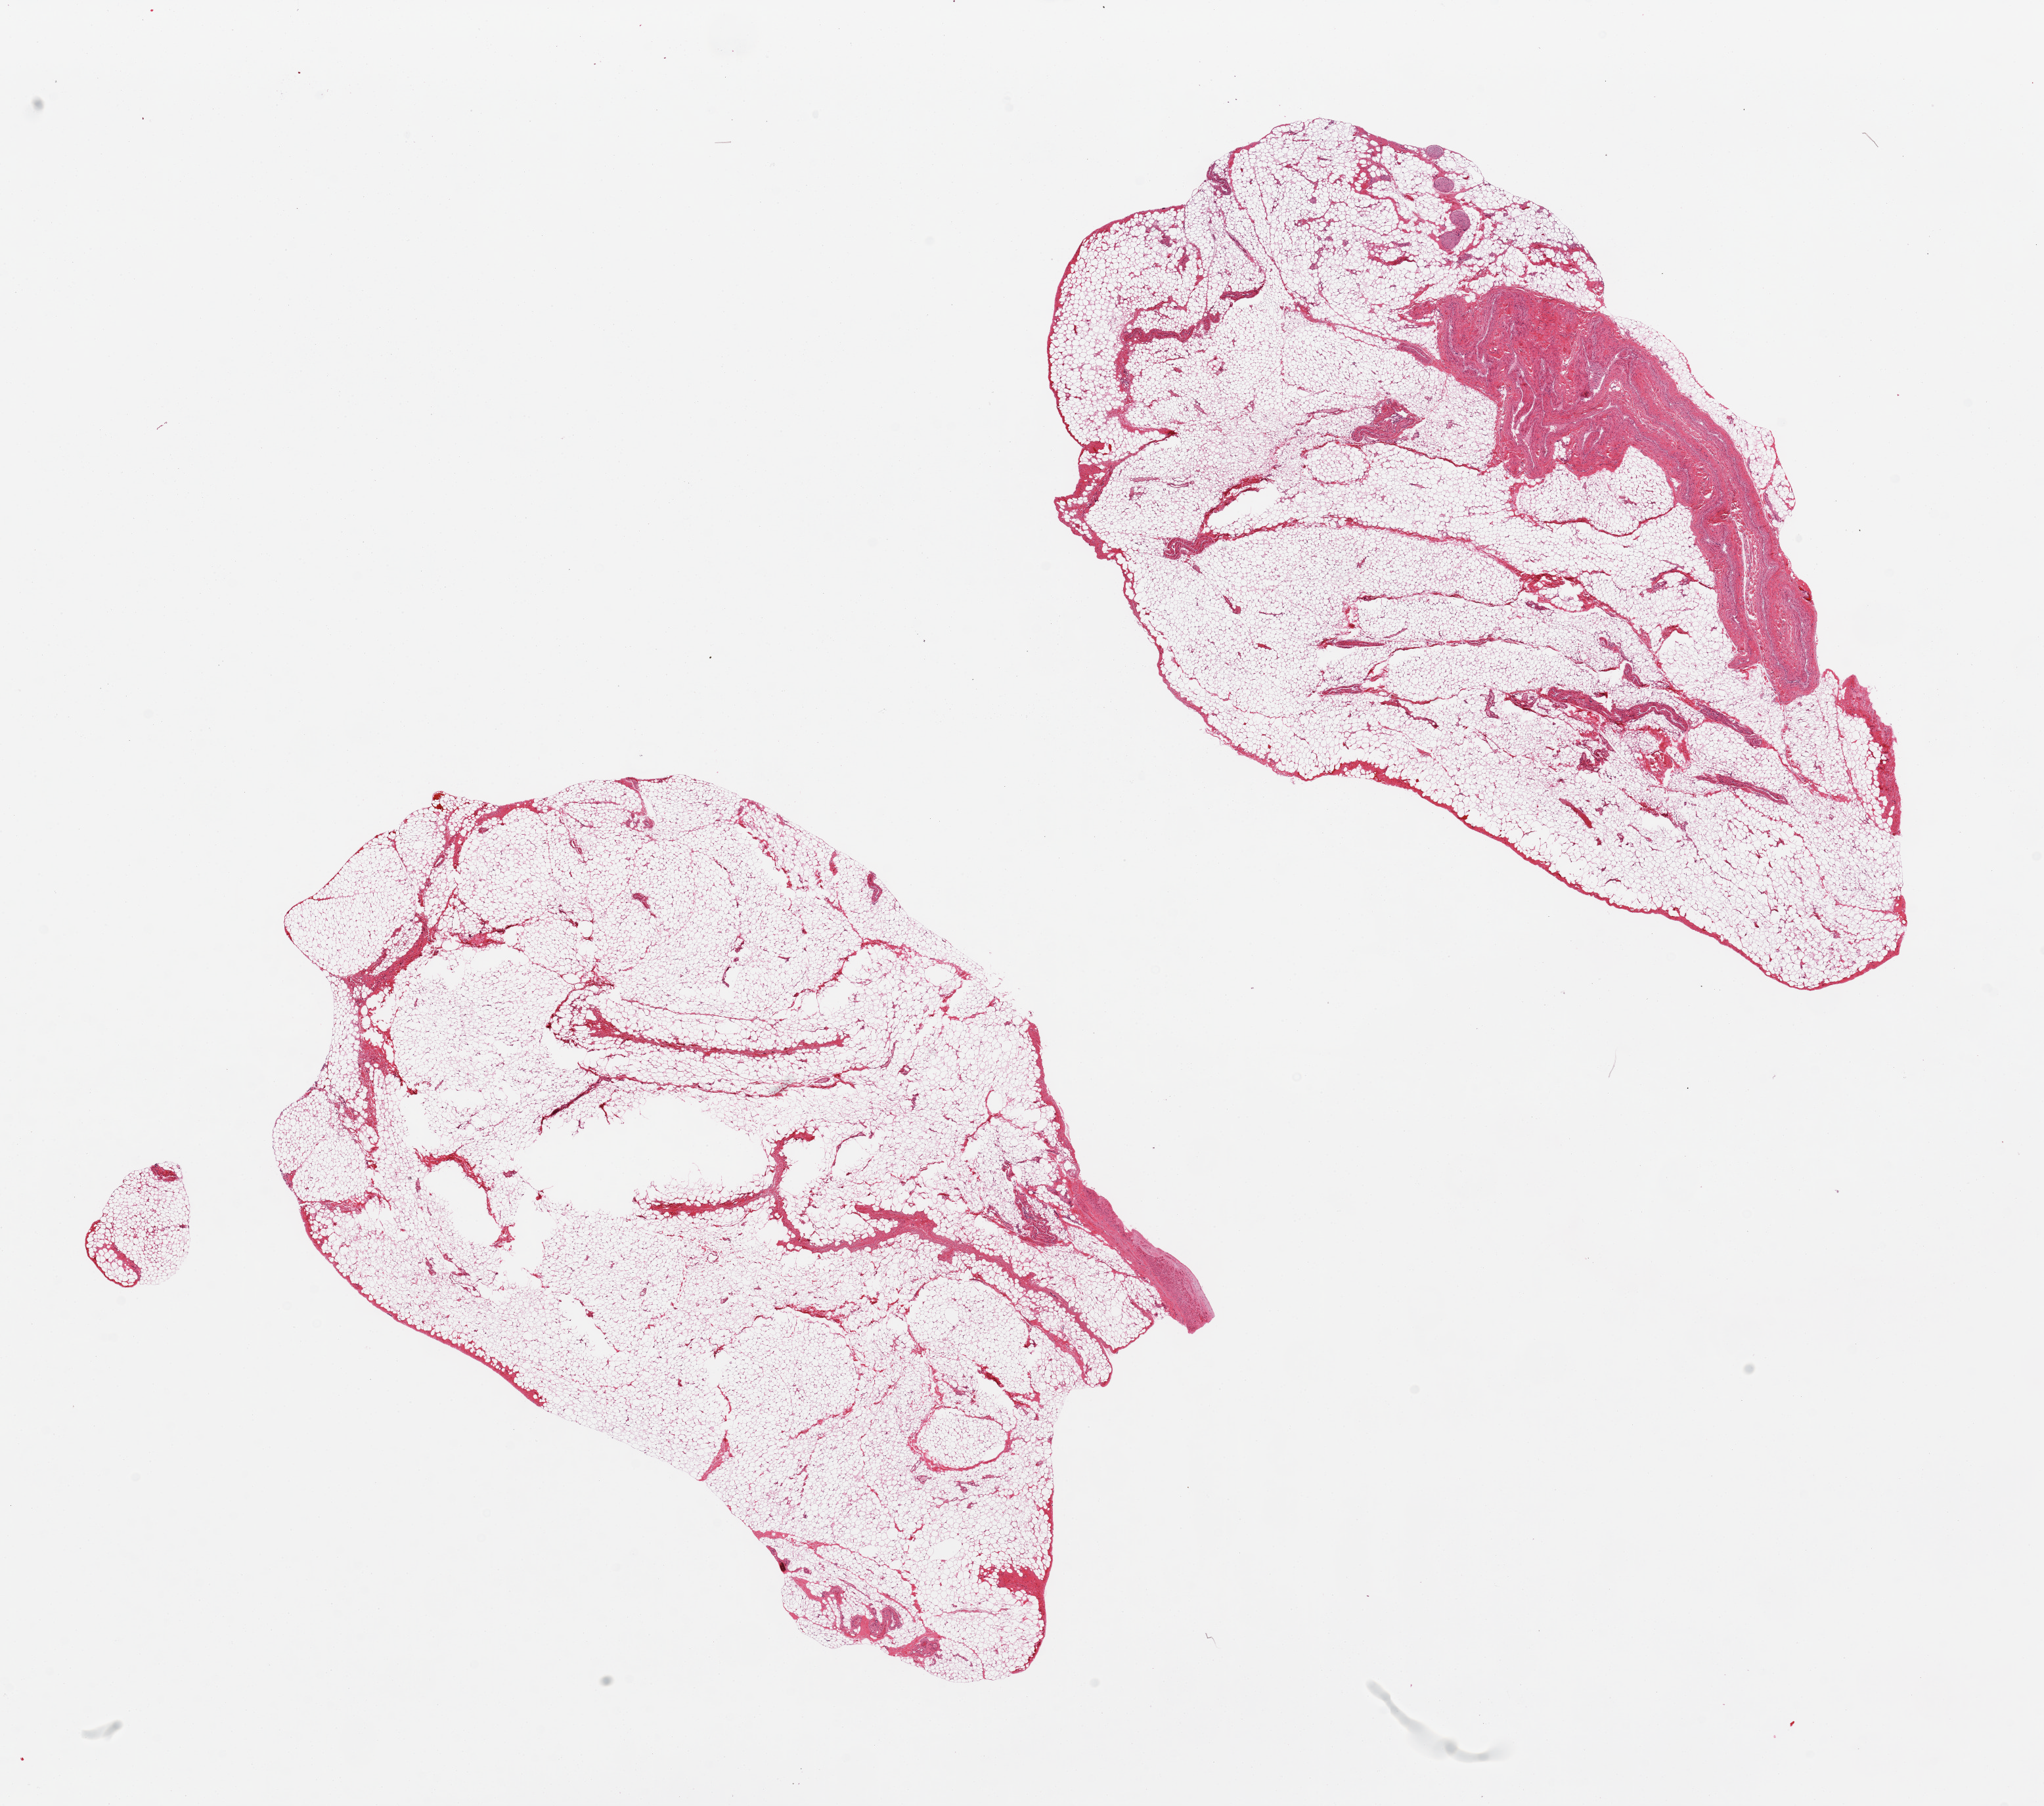
Whole-slide image, hematoxylin and eosin (H&E) stain, brightfield, shown as a low-resolution overview of the whole scanned area (about 24.6 x 21.7 mm). PAXgene-fixed paraffin-embedded (PFPE) section. Target tissue: omentum. Tissue donor sample. Female donor.
* pathologist's review note for this sample: 2 pieces, prominent vessel/fascia/nerve tissue, ~20% of sections